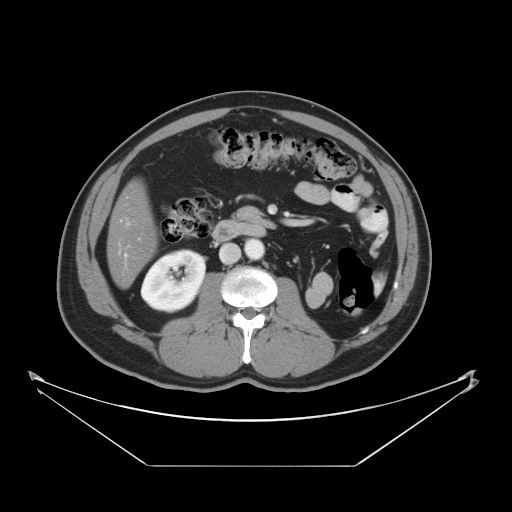
Contrast-enhanced abdominal CT, one axial slice. Position 14 of 46 along the scan axis. 120 kVp. Soft-tissue window (W 400 / L 40 HU). 512 × 512 image matrix, field of view 465 × 465 mm. Male patient, age 57 years. Case-level facts recorded for this patient, not image findings: diagnosis: colorectal cancer liver metastases, imaged before liver resection; multiple liver metastases: no; largest metastasis: 3.3 cm; chemotherapy before resection: yes.
Annotated regions visible in this slice (outlined manually by an expert reader):
- liver: box from (x=108, y=184) to (x=155, y=286) px
- planned liver remnant (the part of the liver to remain after resection): (x=108, y=184)–(x=155, y=286)